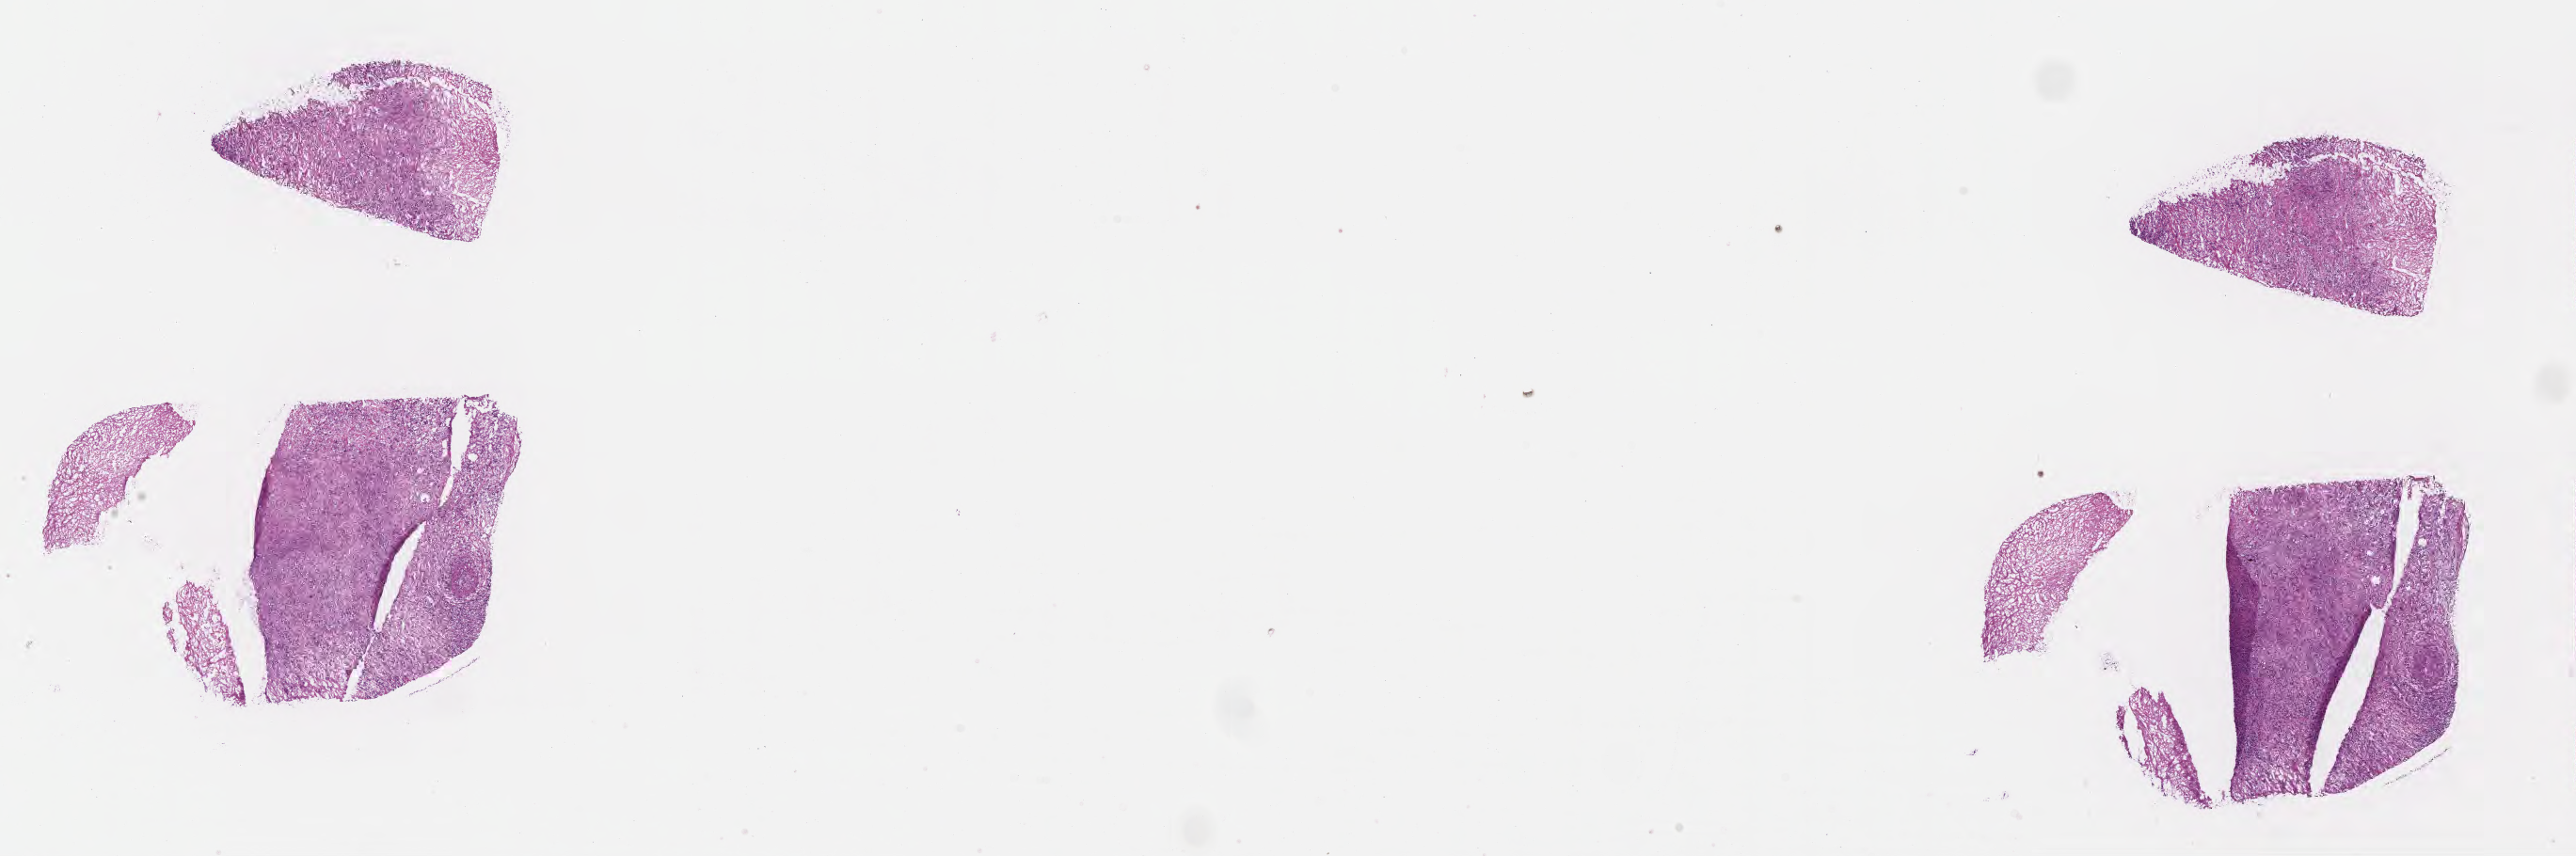
Whole-slide image, H&E stain, low-resolution overview of the scanned area, about 22.1 x 7.4 mm; frozen section (tissue freezing medium); specimen: primary tumor; site: head of pancreas. Male, age 48 years at initial diagnosis. Tumor grade: G3 (poorly differentiated). Pathologist review of this section (percent, as recorded): tumor cells 70%, tumor nuclei 75%, stromal cells 30%, necrosis 0%, normal cells 0%. Infiltration values recorded for this section: lymphocyte infiltration 0%, monocyte infiltration 0%, neutrophil infiltration 0%.
- AJCC pathologic stage: Stage IV
- diagnosis: Infiltrating duct carcinoma, NOS